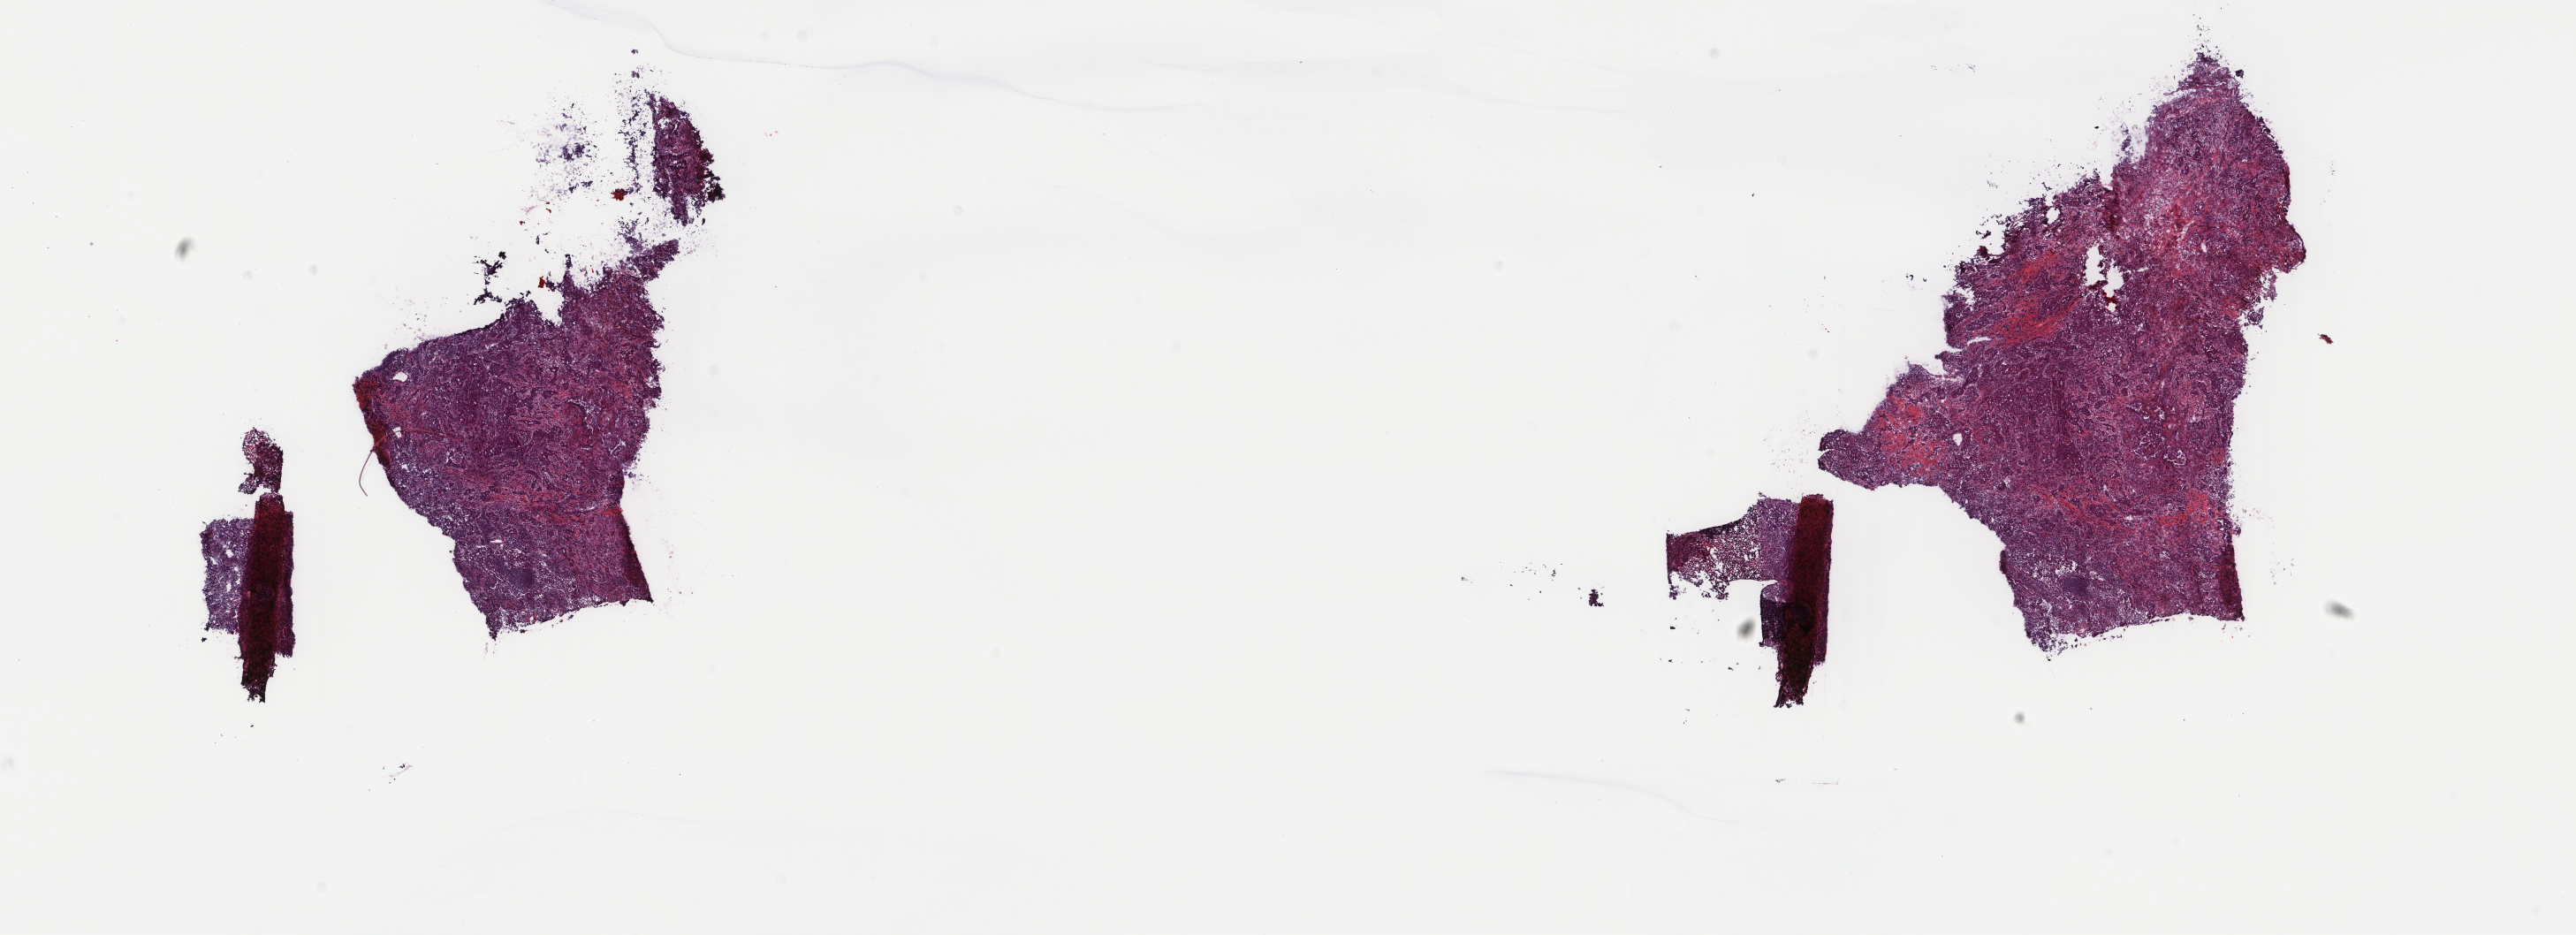
Whole-slide histology image, Hematoxylin and eosin (H&E) stained — a low-resolution overview of the entire scanned area, about 23.1 x 8.4 mm, frozen section from the top of the tissue portion, primary tumour sample from the lung. Patient: male, age at initial diagnosis 59 years. Pathologist review of this section (percent, as recorded): tumour cells 75%, tumour nuclei 75%, normal cells 0%, stromal cells 25%, necrosis 0%. Inflammatory infiltration, as recorded: lymphocyte infiltration 4%, monocyte infiltration 2%, neutrophil infiltration 3%.
- AJCC pathologic stage: IB
- histologic diagnosis: Adenocarcinoma, NOS (upper lobe, lung)